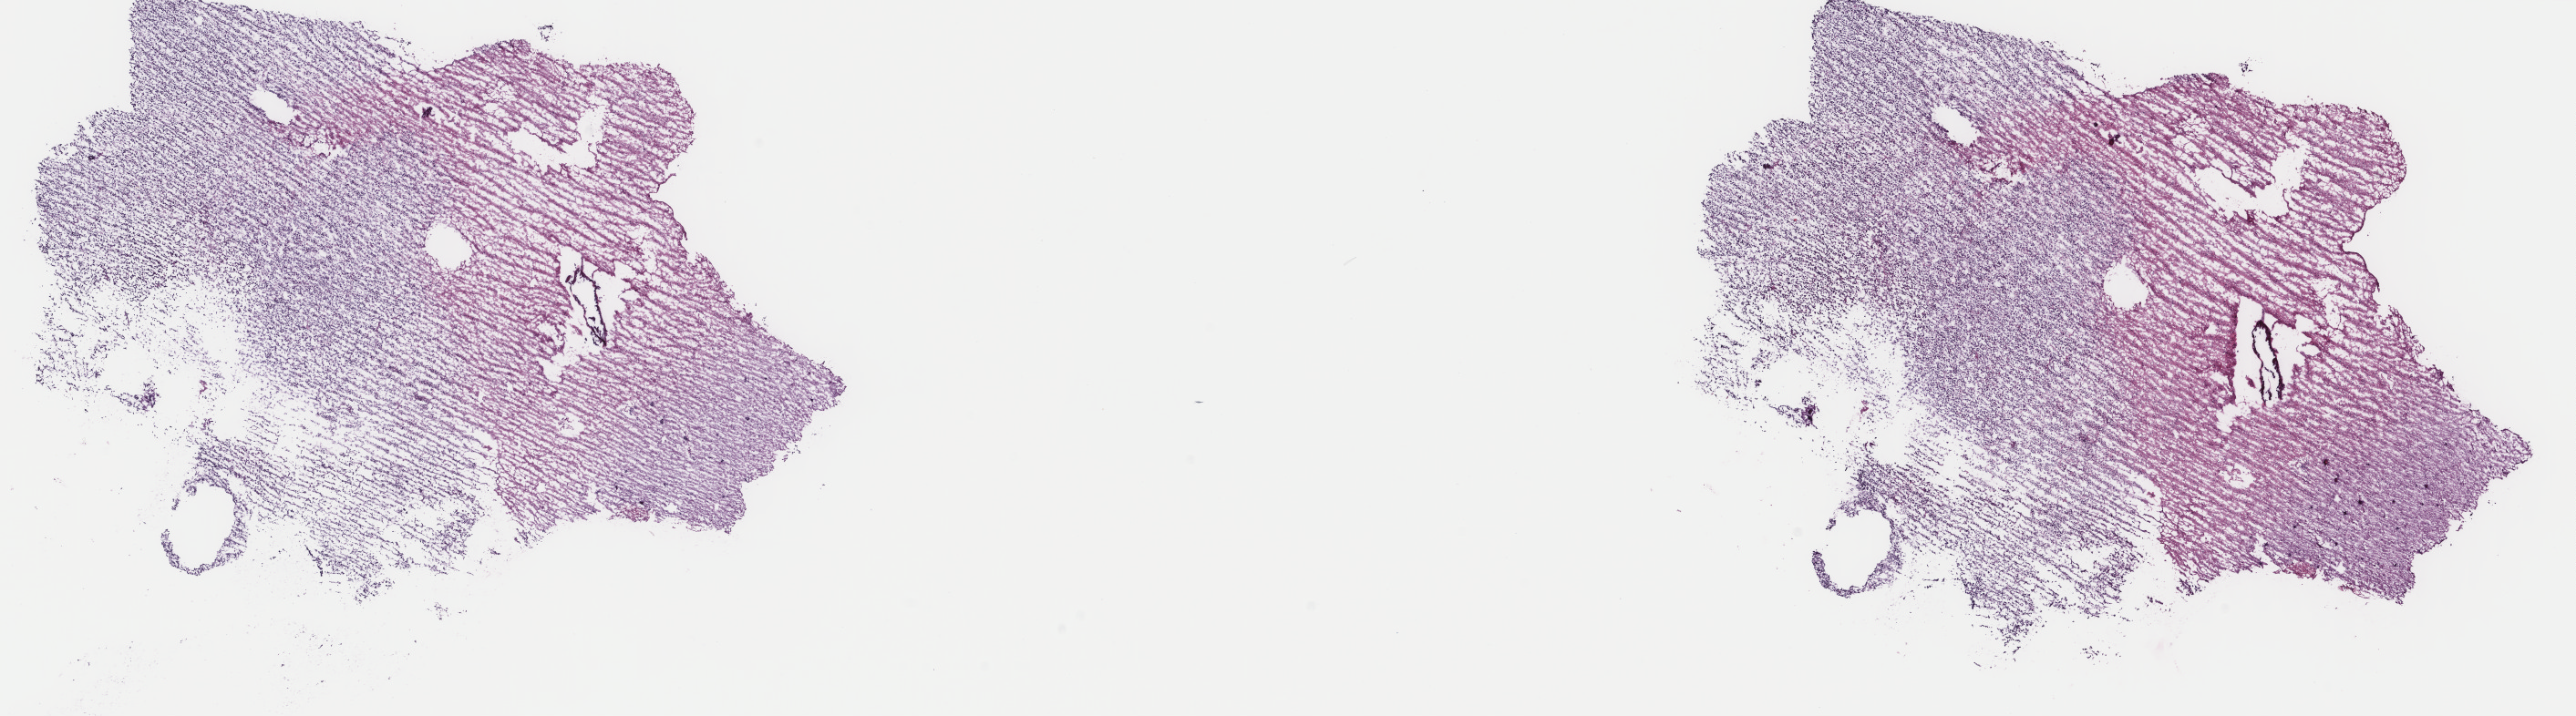
H&E-stained whole-slide image, shown as a low-resolution overview of the whole scanned area (about 22.4 x 6.2 mm, from a 40x scan). Frozen section from the top of the tissue portion. Sample: primary tumour, brain. Female, age 64 years at initial diagnosis. Histologic grade: G3 (poorly differentiated). Composition of this section per pathologist review: tumour cells 70%, tumour nuclei 90%, normal cells 5%, stromal cells 25%, necrosis 0%. Infiltration values recorded for this section: lymphocyte infiltration 0%, monocyte infiltration 0%, neutrophil infiltration 0%.
Pathologic diagnosis: Oligodendroglioma, anaplastic (cerebrum). Laterality: left.